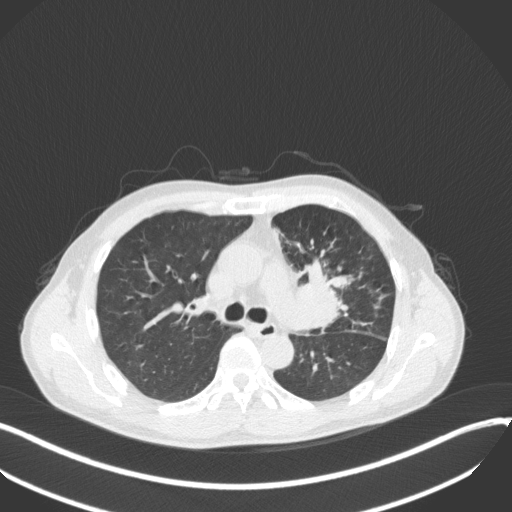
Chest CT, one axial slice. Position 217 of 411 along the scan axis. 120 kVp. Lung window (W 1500 / L -600 HU). 512 × 512 image matrix. Patient: male, 56 years. From the clinical record (not read from this slice): clinical TNM (as recorded): T2a N0 M0.
Annotated regions visible in this slice (rectangle marked by the reading radiologist):
- lung tumour (recorded histology: squamous cell carcinoma): bounding box (x1, y1, x2, y2) in pixels: (294, 252, 355, 333)